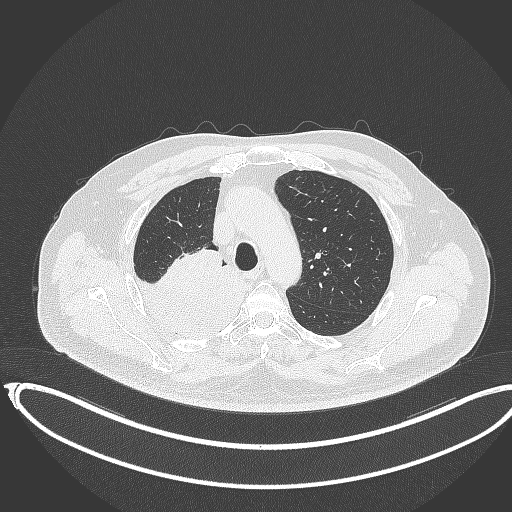
Chest CT, one axial slice. Slice 270 of 403 in the series (ordered by position). 120 kVp. Lung window (W 1500 / L -600 HU). 512 × 512 image matrix, field of view 436 × 436 mm. Male patient, age 68 years. From the clinical record (not read from this slice): clinical TNM (as recorded): T2a N0 M0.
Structures marked on this image (rectangle marked by the reading radiologist):
- lung tumour (recorded histology: adenocarcinoma): bounding box <129,251,250,336> (left, top, right, bottom; pixels)